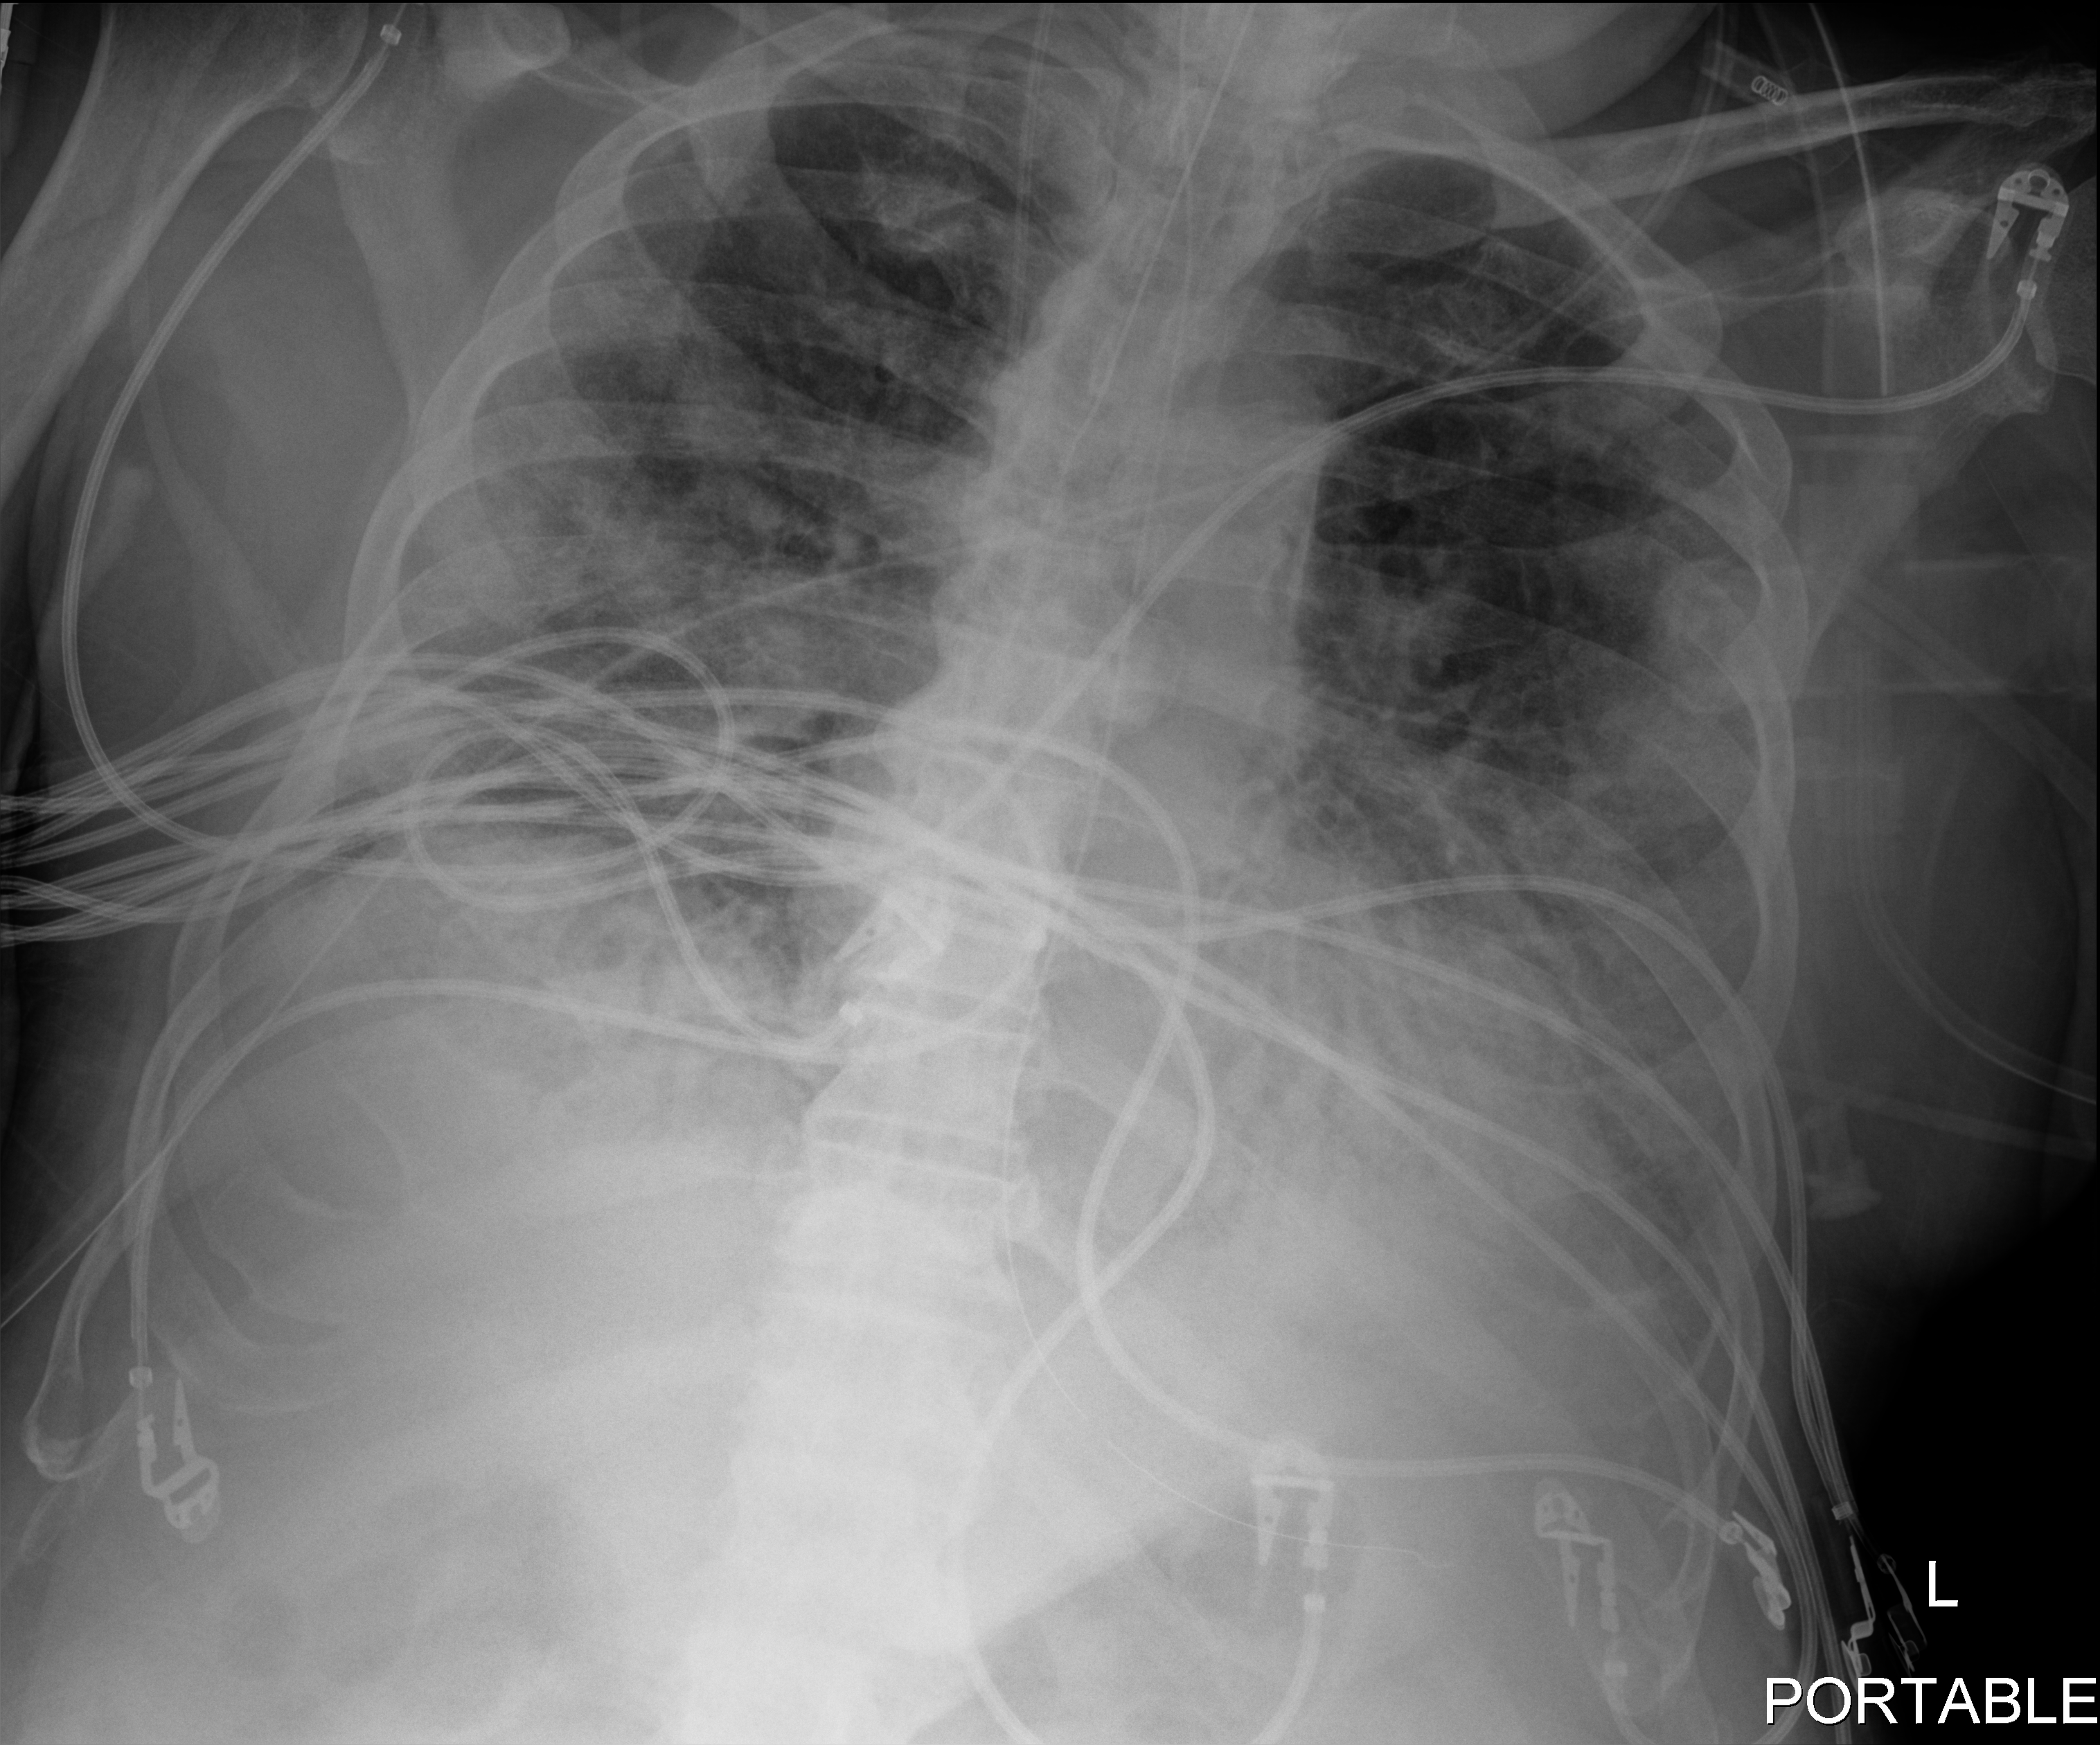
Bedside chest radiograph (digital radiography), anteroposterior (AP) projection. Patient hospitalised with COVID-19; male, aged 75–90 years.
From the hospital-stay record, not from the radiograph (when in the stay this image was taken is not recorded): mechanically ventilated during this hospital stay: yes; hypertension (admission record): yes.